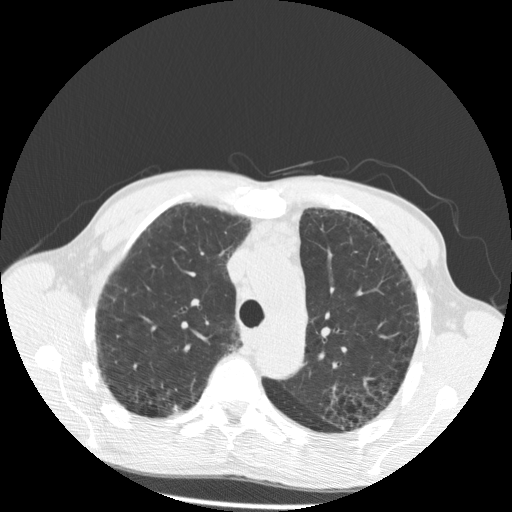
Chest CT (low-dose screening protocol), one axial image; baseline screening round; lung window (W 1500 / L -600 HU); standard (soft-tissue) reconstruction kernel (STANDARD); slice 134 of 181 in the series. Male, age 60 years at enrolment.
• Lesion marked by an expert reader, bounding box [x1, y1, x2, y2] px = [163, 397, 188, 419].
• Screening reader's record for this exam (one nodule recorded; not confirmed to be the boxed lesion): non-calcified nodule or mass ≥4 mm, right lower lobe, 6 × 6 mm, spiculated (stellate) margins, soft tissue attenuation.
• Official screen result: positive, change unspecified: nodule(s) >= 4 mm or enlarging nodule(s), mass(es), or other non-specific abnormalities suspicious for lung cancer.
• Later outcome: lung cancer diagnosed 688 days after this screen — squamous cell carcinoma, NOS, right upper lobe, well differentiated (G1), stage IA (AJCC 6th edition), 15 mm at pathology.